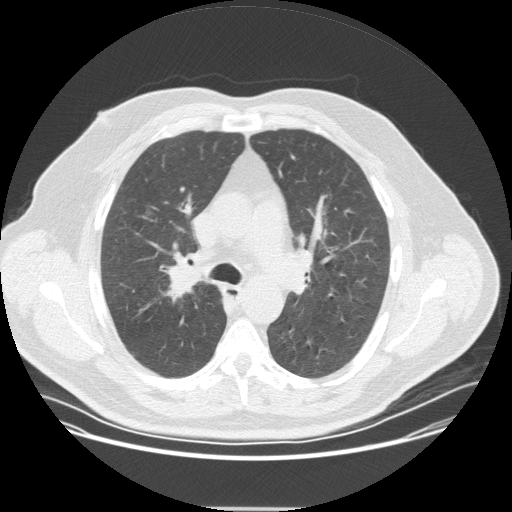
Low-dose screening chest CT, one axial slice; slice 230 of 351 in the series (ordered by position); reconstruction kernel STANDARD; lung window (W 1500 / L -600 HU); 2.5 mm slice thickness; 512 × 512 image matrix, field of view 419 × 419 mm.
Outlined on this slice (expert manual segmentation):
- lesion 1 (tumor, upper lobe of right lung): bounding box [x1, y1, x2, y2] px = [164, 269, 203, 303]